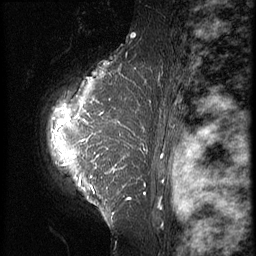
Breast MRI (dynamic contrast-enhanced), one sagittal slice. Slice 48 of 64 in the series (ordered by position). 3 images stored at this slice position (order not interpretable as contrast timing). 1.5 T. TE 4.2 ms, TR 9 ms. 2.5 mm slice thickness. 256 × 256 image matrix, field of view 180 × 180 mm. Female patient, age 39 years. From the clinical record (not read from this slice): setting: breast cancer imaged before/during neoadjuvant chemotherapy; receptor status: HER2-positive.
Structures marked on this image (semi-automatically segmented with operator editing):
- analysis volume of interest (the breast-tissue region the enhancement analysis was run in; not a lesion): box from (x=36, y=47) to (x=149, y=239) px
- tumour enhancement mask (voxels above the 140 % enhancement threshold inside the analysis volume of interest): (x=60, y=101)–(x=145, y=199)